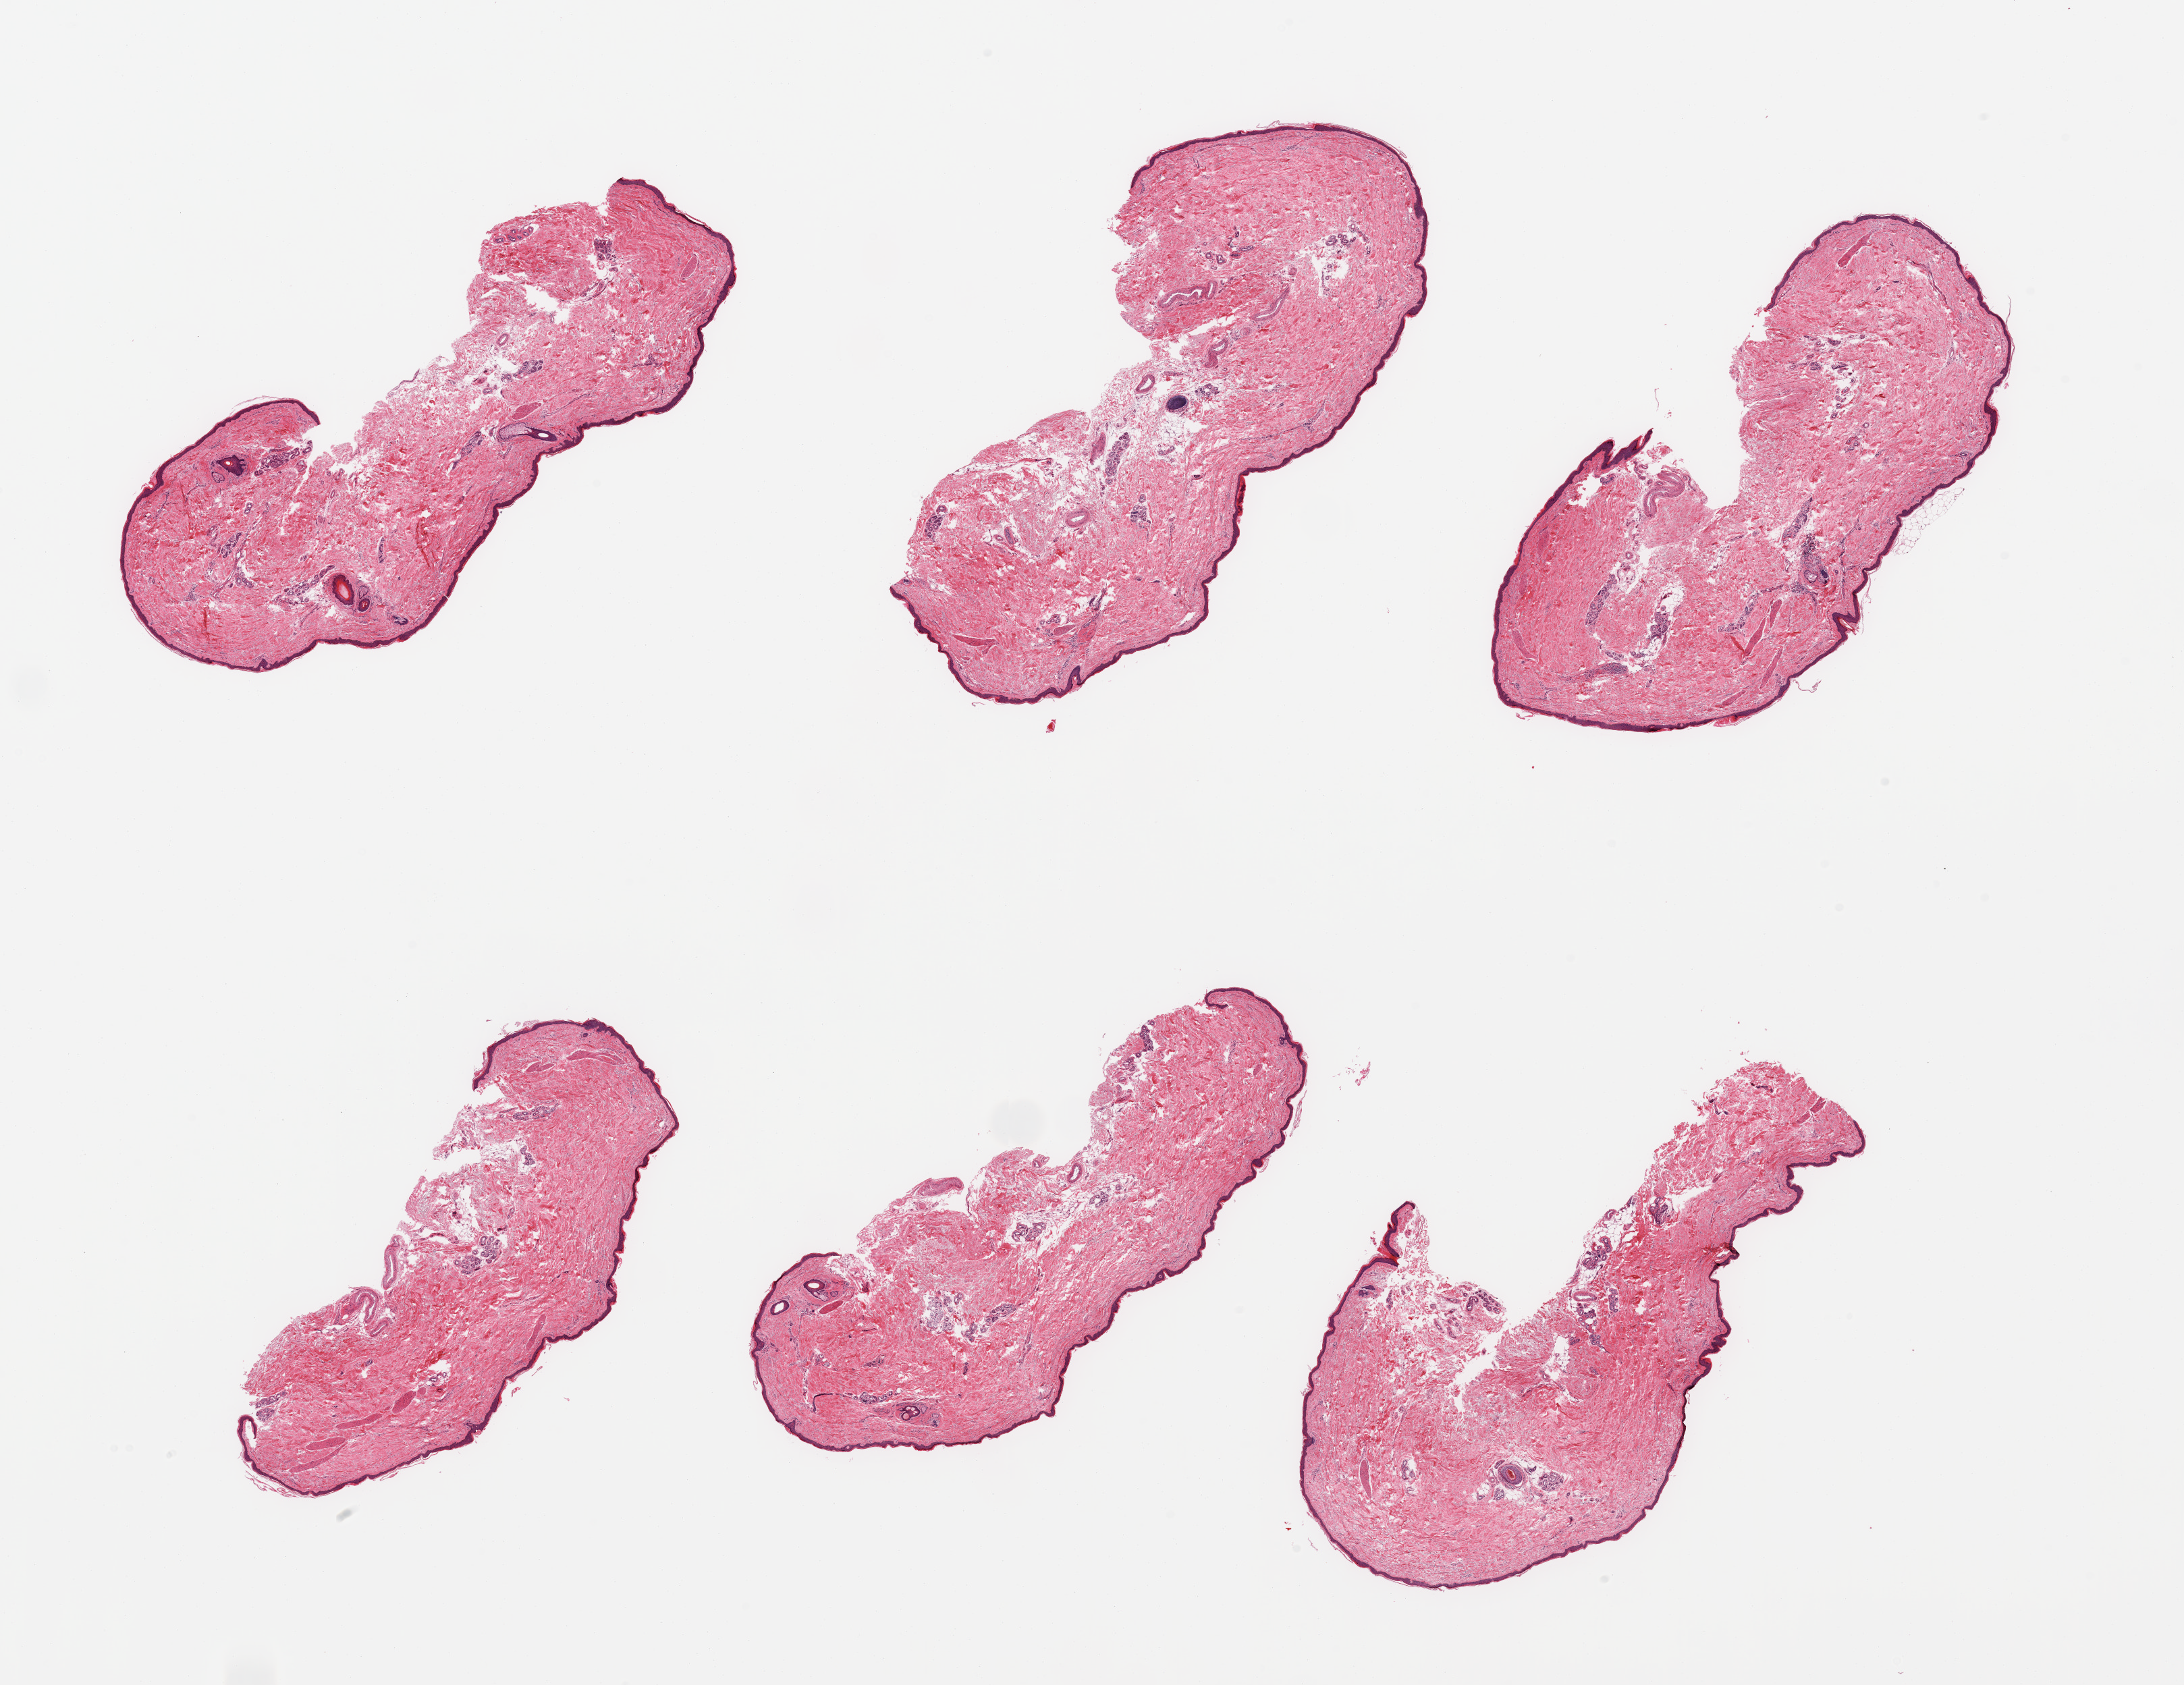
Digitized haematoxylin and eosin-stained section, a low-resolution overview of the entire scanned area, about 25.6 x 19.7 mm (from a 20x scan), PAXgene-fixed, paraffin-embedded tissue, section of skin of lower leg (target tissue), donor tissue sample.
Review note (as recorded): 6 pieces; well trimmed; 5% dermal fat.